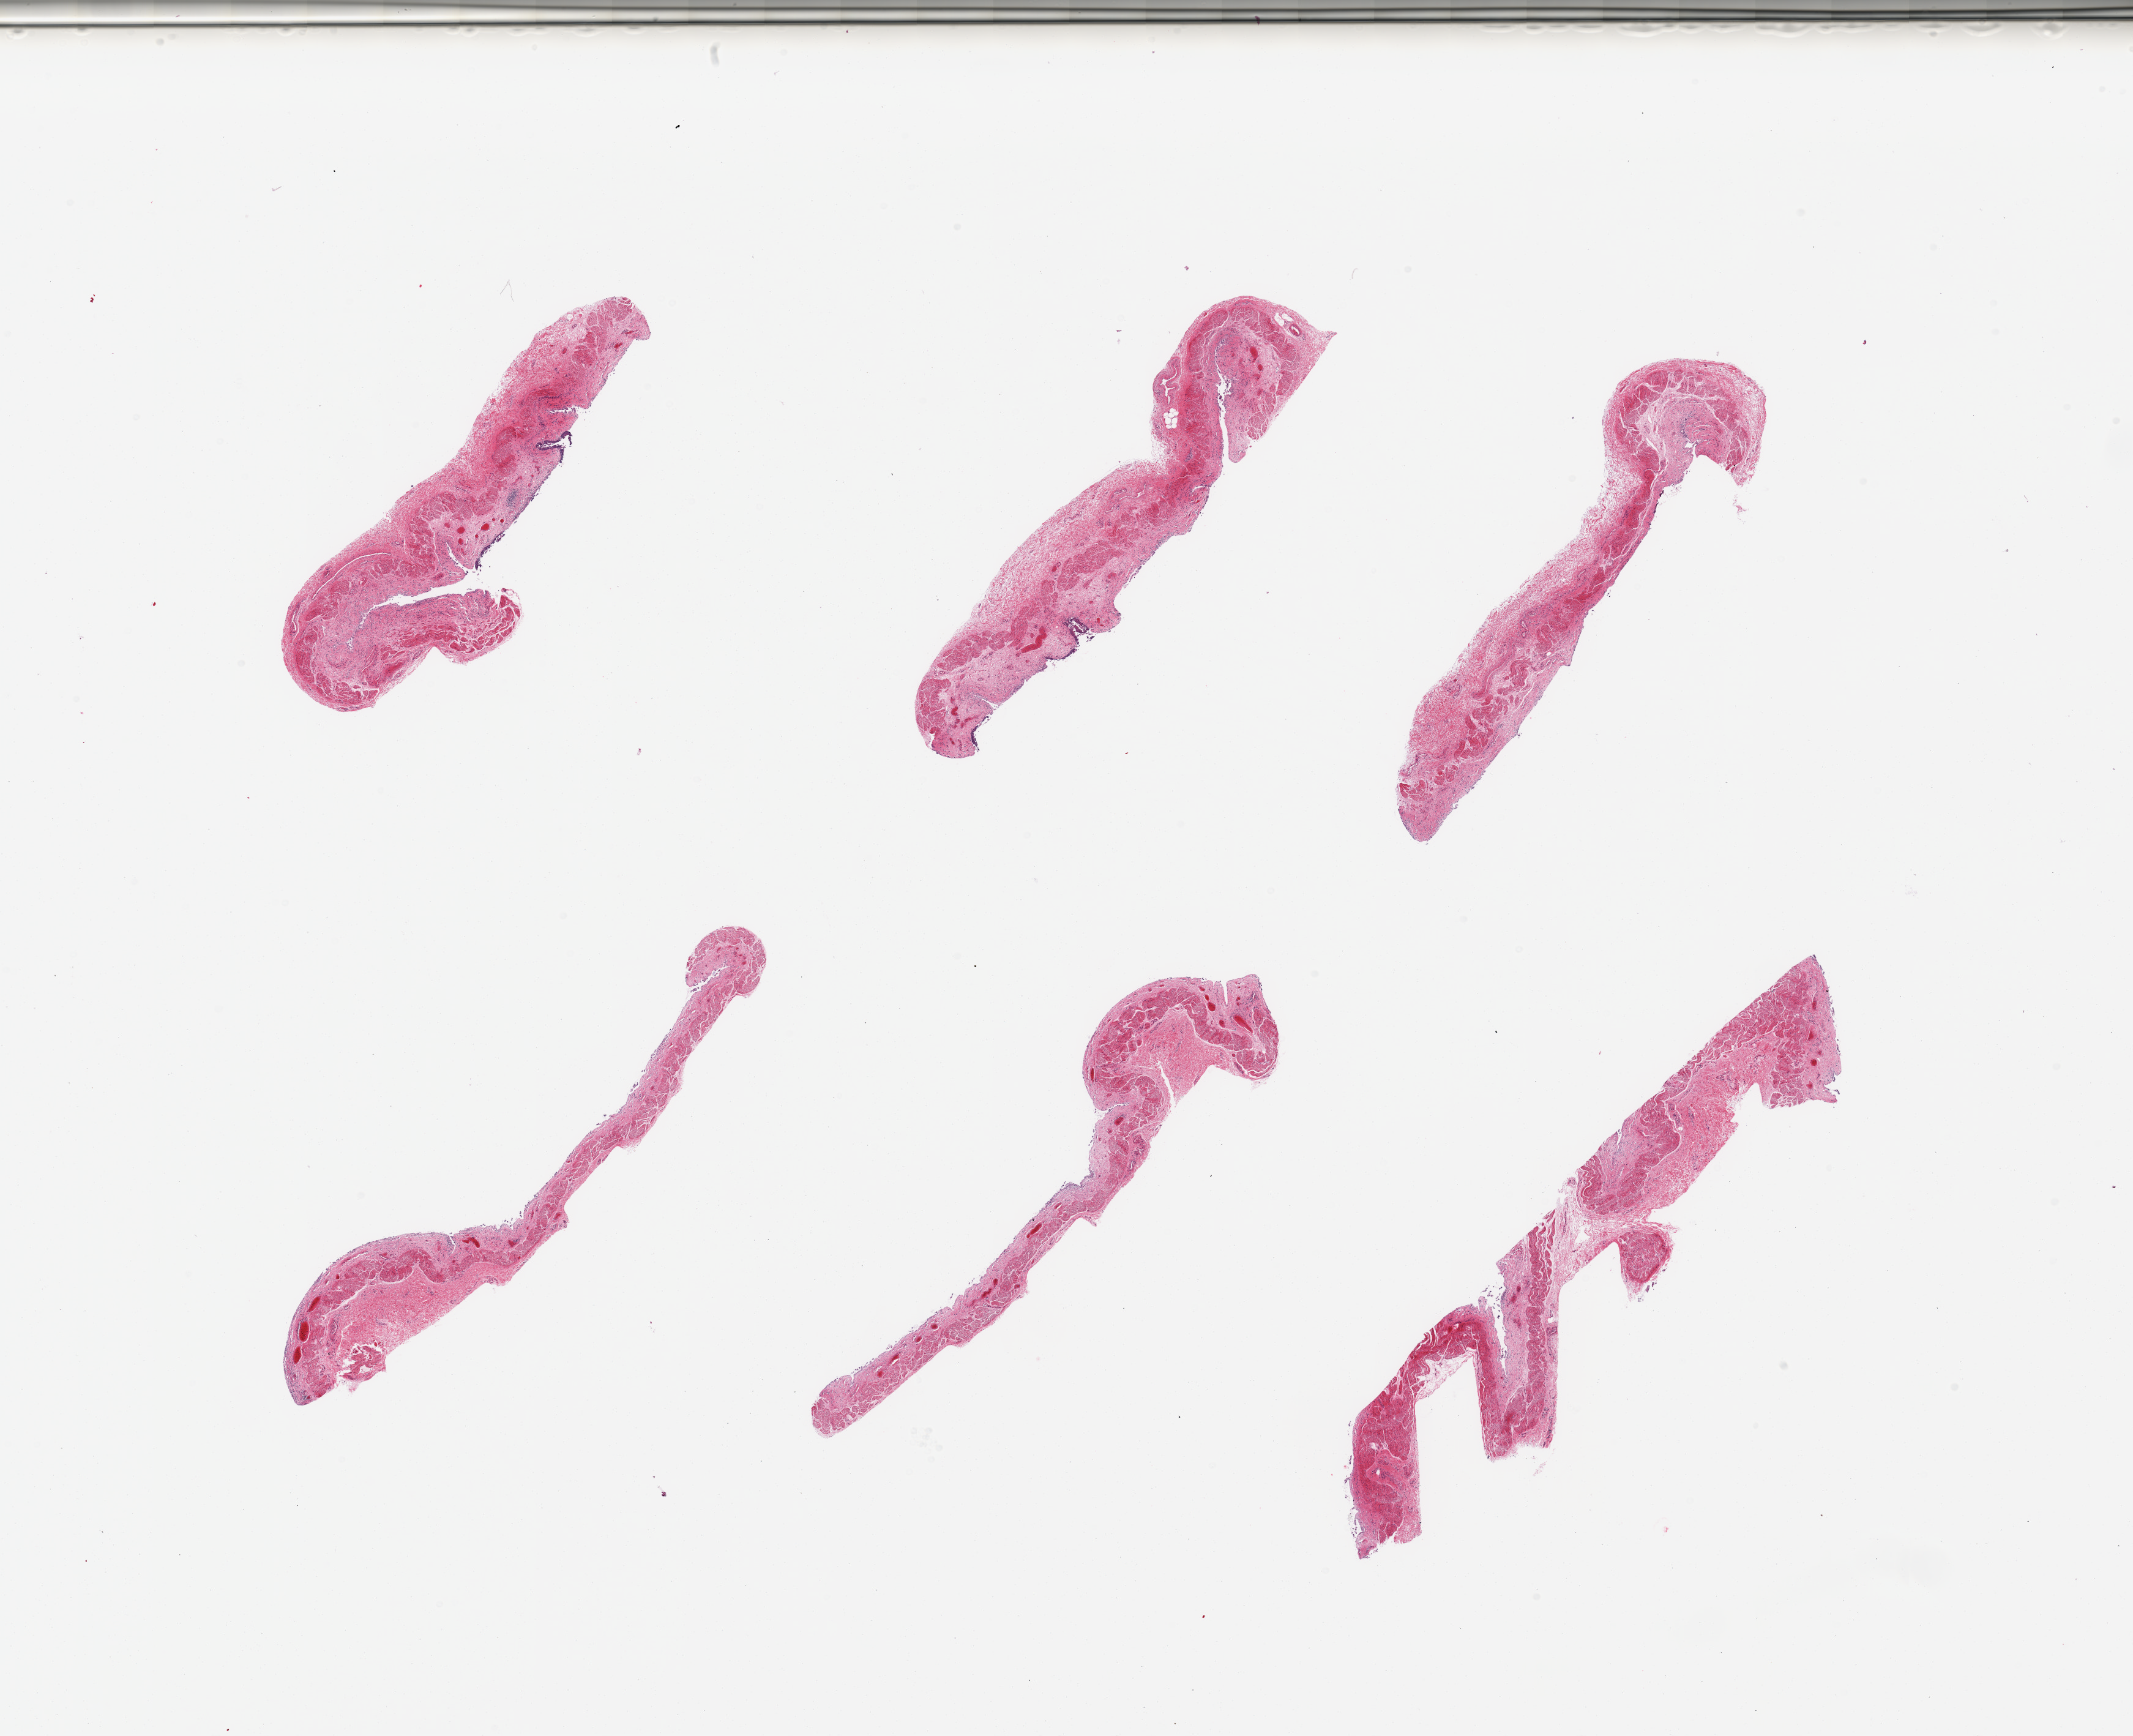
Digitized haematoxylin and eosin-stained section, brightfield — whole scanned area (about 27.6 x 22.4 mm, from a 20x scan) shown as a low-resolution overview; PAXgene-fixed, paraffin-embedded tissue; section of esophageal mucous membrane (target tissue); tissue donor sample. Male donor.
• review note (as recorded): 6 pieces; only remnants of autolyzed mucosa and preserved muscularis mucosa